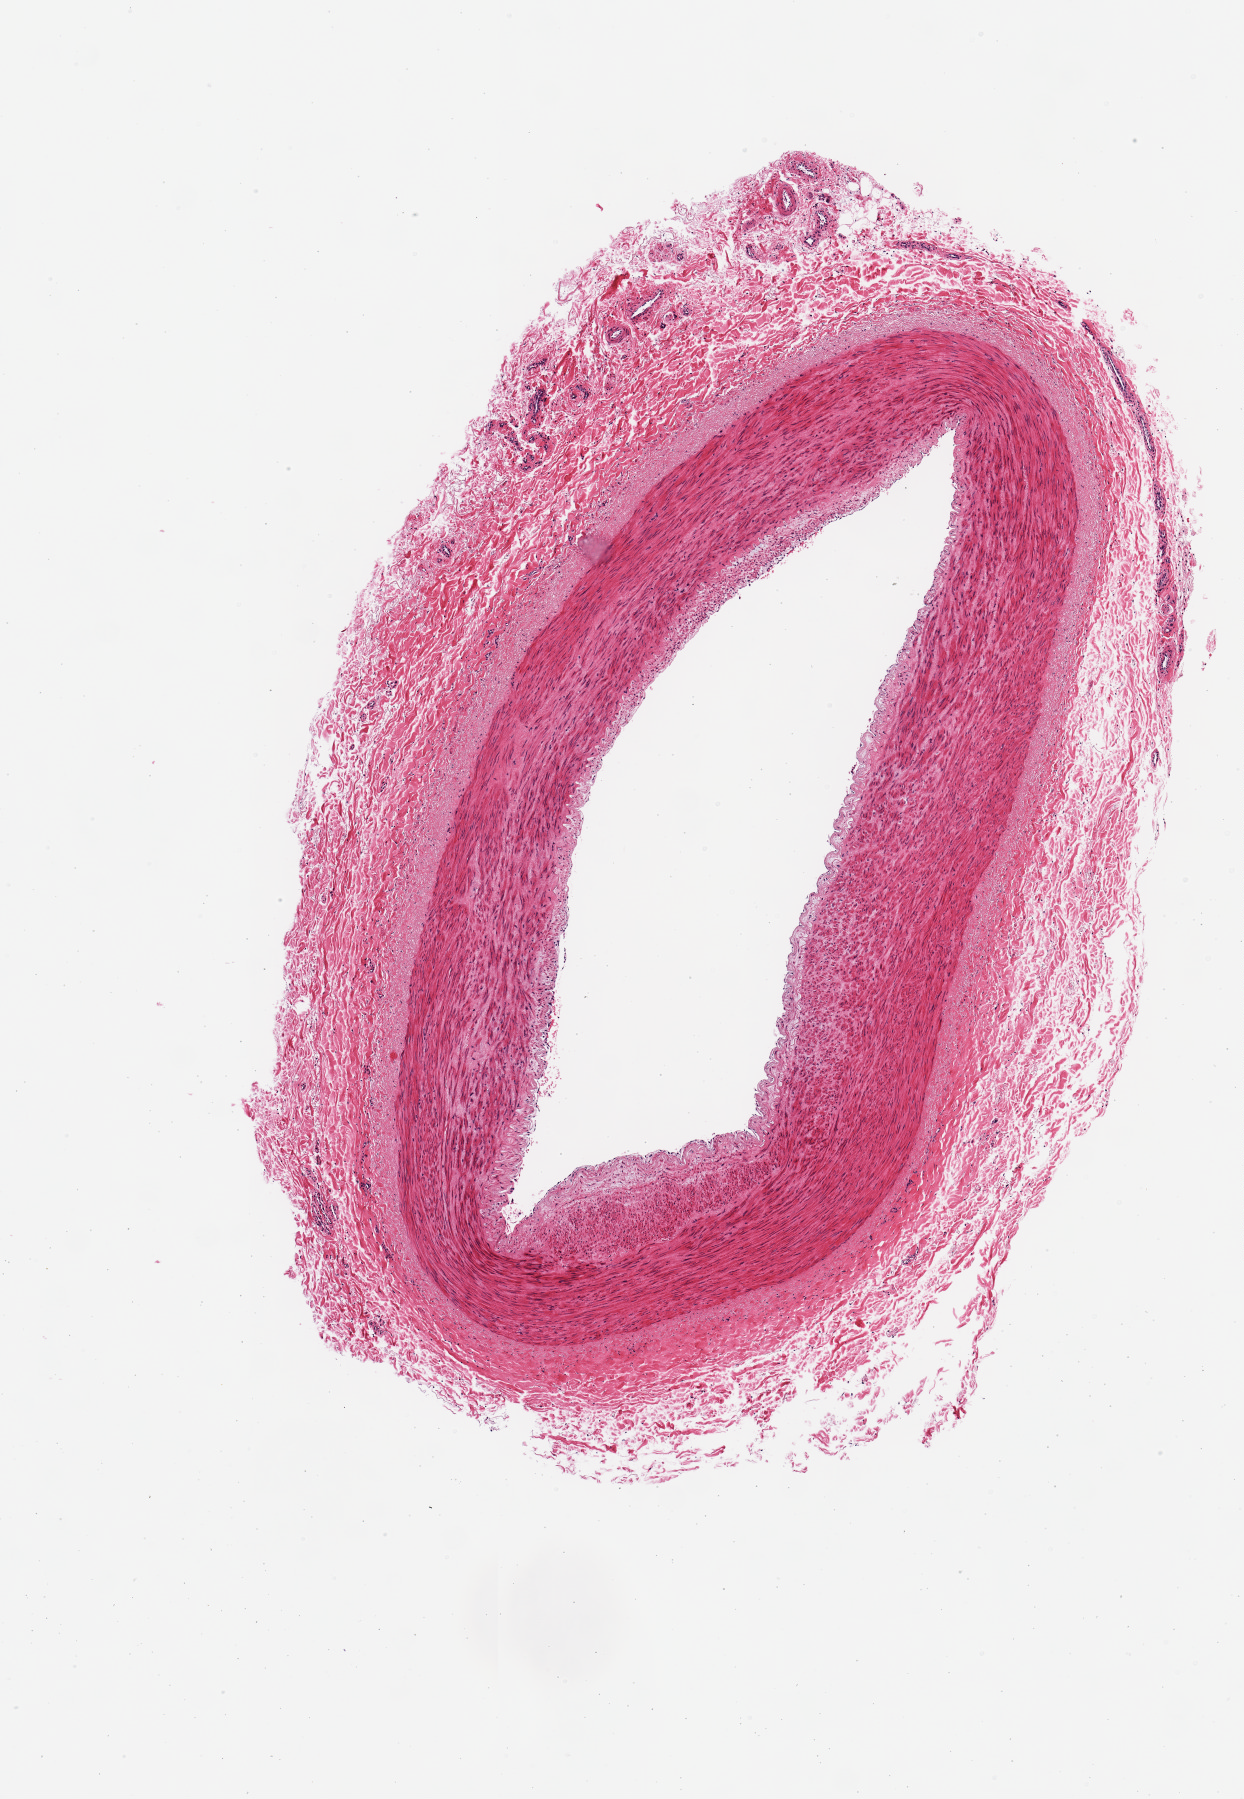
Whole-slide image, haematoxylin and eosin stain, brightfield, shown as a low-resolution overview of the whole scanned area (about 4.9 x 7.1 mm), PAXgene-fixed paraffin-embedded (PFPE) section, target tissue: tibial artery, donor tissue sample. Donor sex: female.
- reviewer comment on this tissue sample: 1 piece; artery not nerve; well trimmed